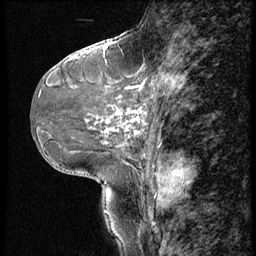
Breast MRI (dynamic contrast-enhanced), one sagittal slice. Slice 25 of 56 in the series (ordered by position). 3 images stored at this slice position (order not interpretable as contrast timing). 1.5 T. TE 4.2 ms, TR 9 ms. 2.5 mm slice thickness. 256 × 256 image matrix, field of view 180 × 180 mm. Female patient, age 46 years. From the clinical record (not read from this slice): setting: breast cancer imaged before/during neoadjuvant chemotherapy; receptor status: HER2-positive.
Structures marked on this image (semi-automatically segmented with operator editing):
- analysis volume of interest (the breast-tissue region the enhancement analysis was run in; not a lesion): bounding box <79,68,190,143> (left, top, right, bottom; pixels)
- tumour enhancement mask (voxels above the 140 % enhancement threshold inside the analysis volume of interest): <105,86,175,135>